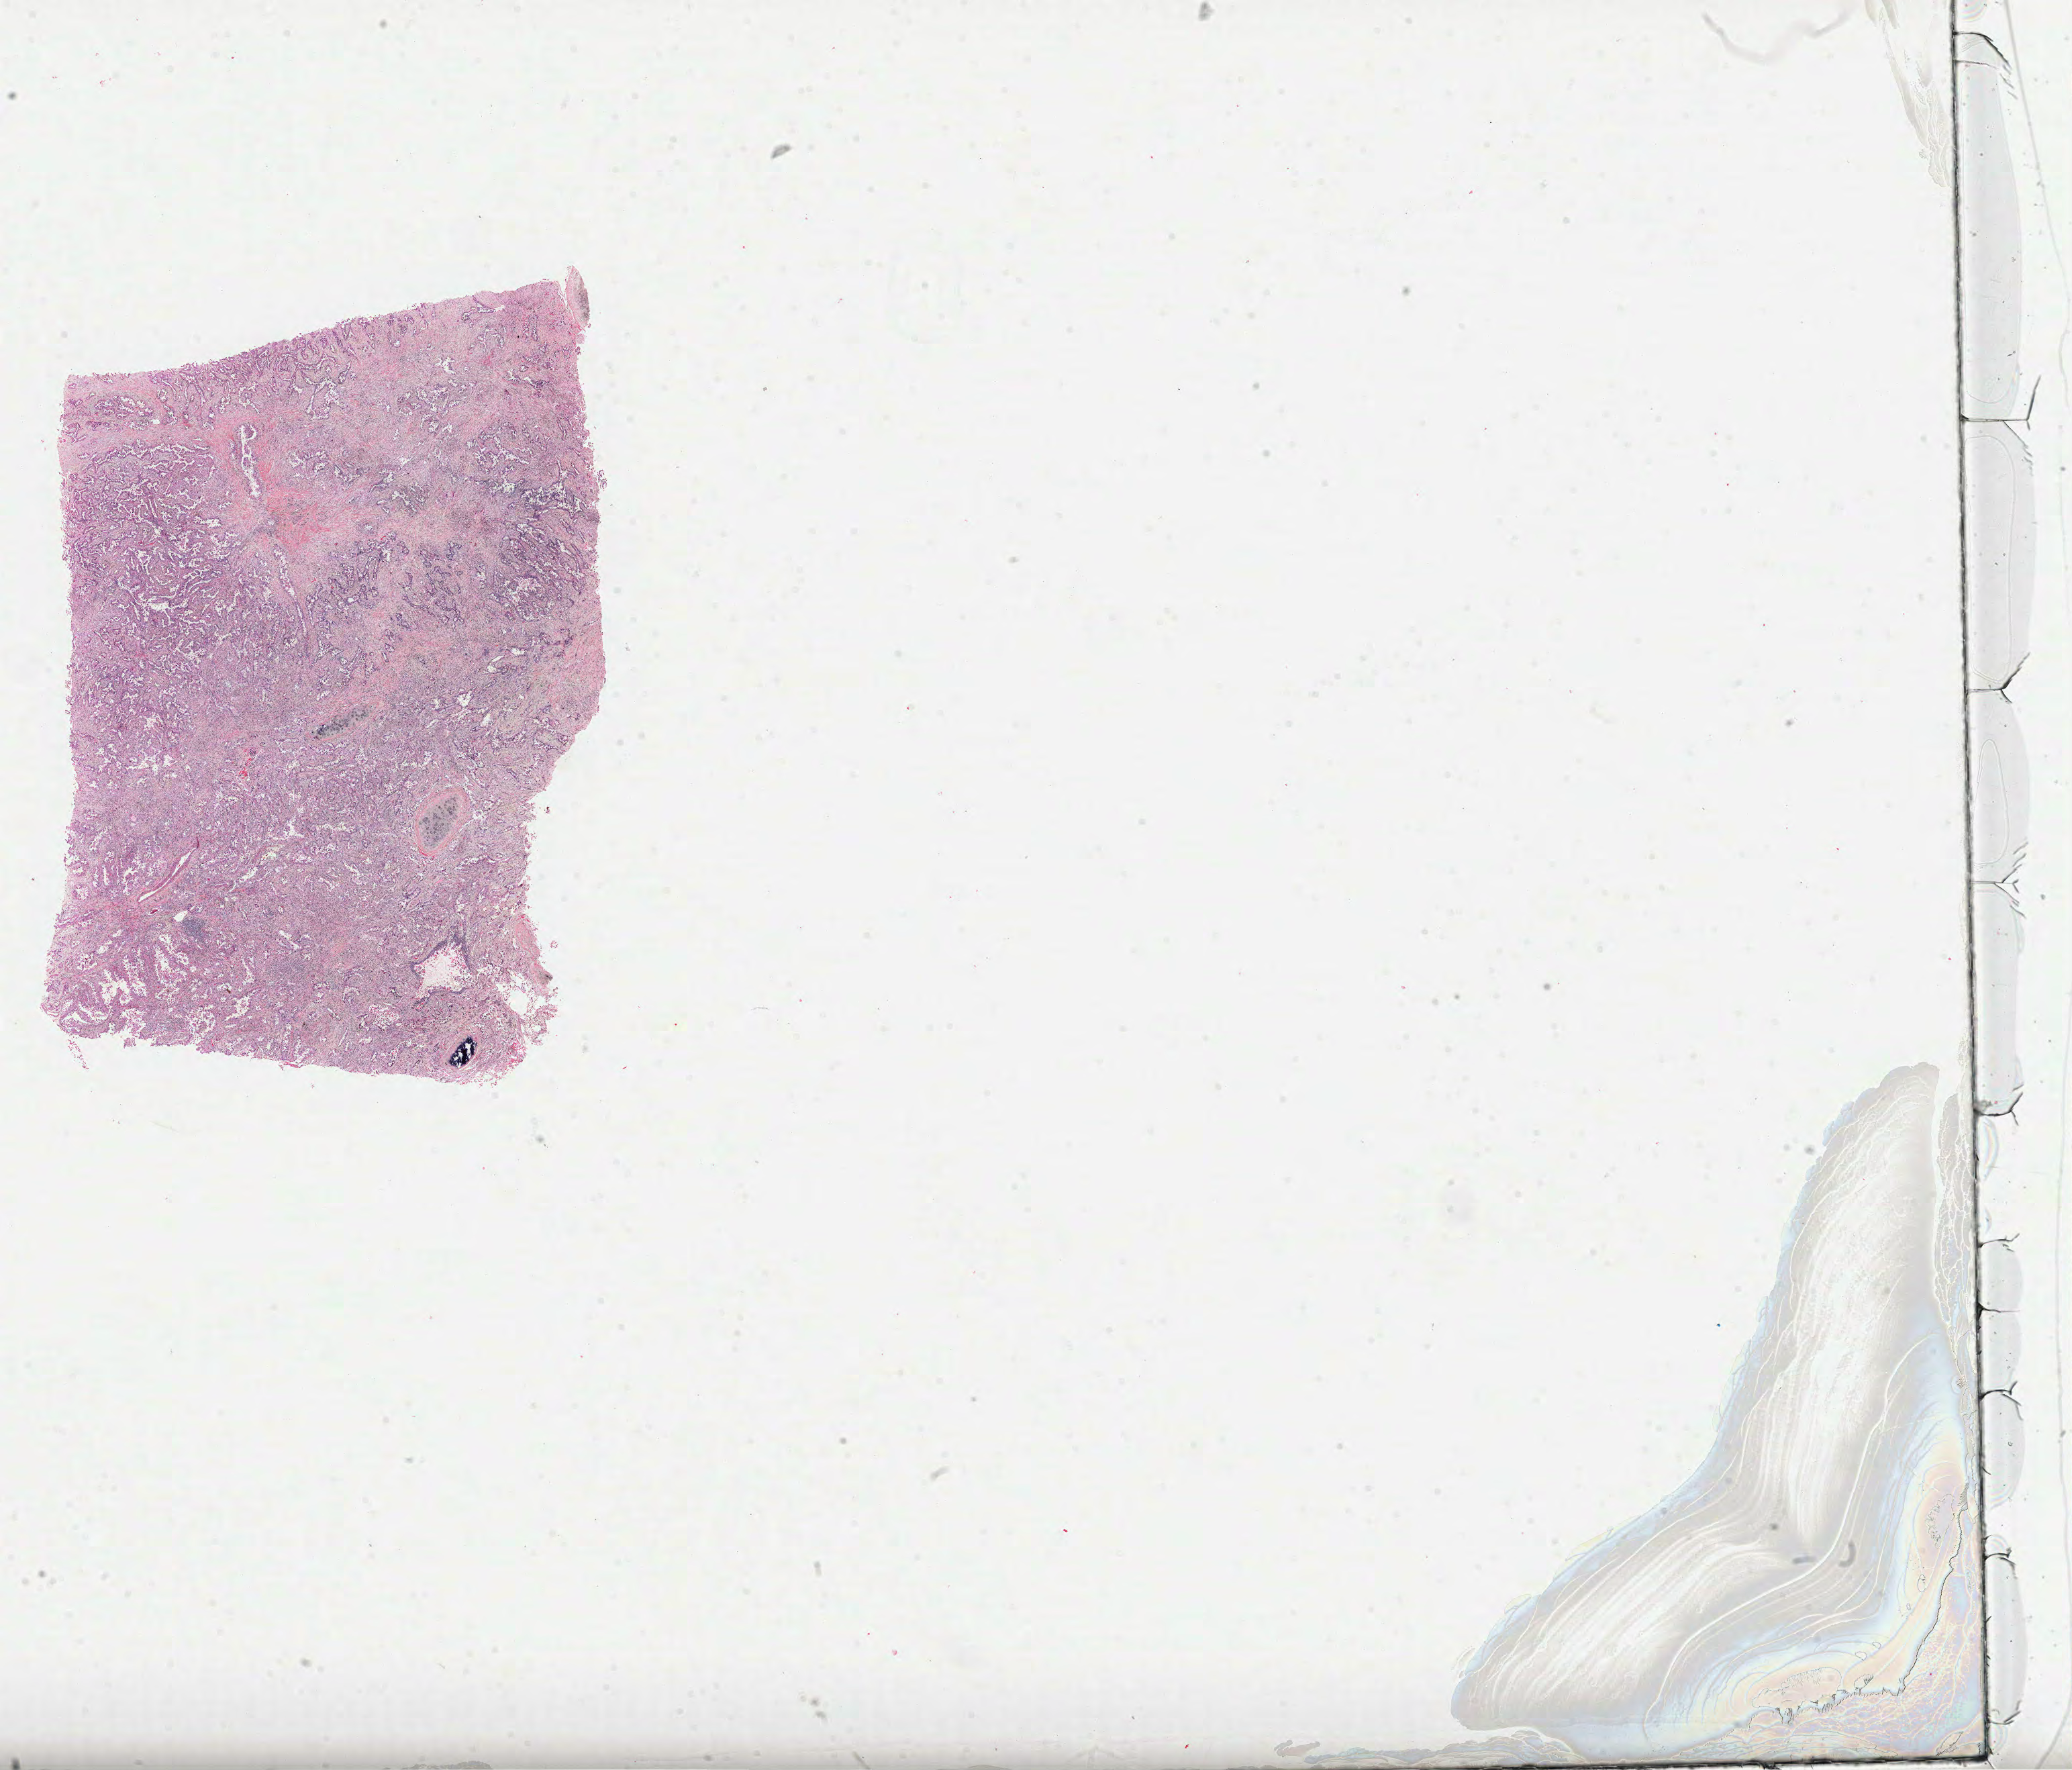
Whole-slide histology image, H&E — a low-resolution overview of the entire scanned area, about 24.9 x 21.3 mm (slide scanned at 40x); formalin-fixed paraffin-embedded (FFPE) diagnostic section; primary tumour sample from the lung. Patient: female, age at initial diagnosis 65 years.
TNM: T2 N1 M0. AJCC pathologic stage: IIB. Pathologic diagnosis: Adenocarcinoma, NOS (upper lobe, lung).